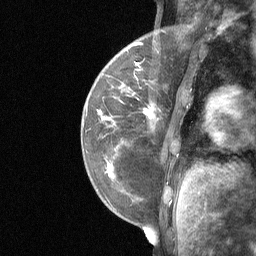
Breast MRI (dynamic contrast-enhanced), one sagittal slice; slice 16 of 64 in the series (ordered by position); dynamic contrast-enhanced study with each time point stored as its own series, time point 2 of 3 at this slice position (early post-contrast, ordered by acquisition time); 1.5 T; TE 4.8 ms, TR 27 ms; 256 × 256 image matrix, field of view 200 × 200 mm. Patient: female, 34 years. From the clinical record (not read from this slice): setting: breast cancer imaged before/during neoadjuvant chemotherapy; receptor status: HR-positive, HER2-negative.
Outlined on this slice (semi-automatically segmented with operator editing):
- analysis volume of interest (the breast-tissue region the enhancement analysis was run in; not a lesion): bounding box [x1, y1, x2, y2] px = [92, 50, 188, 185]
- tumour enhancement mask (voxels above the 90 % enhancement threshold inside the analysis volume of interest): [99, 63, 150, 116]